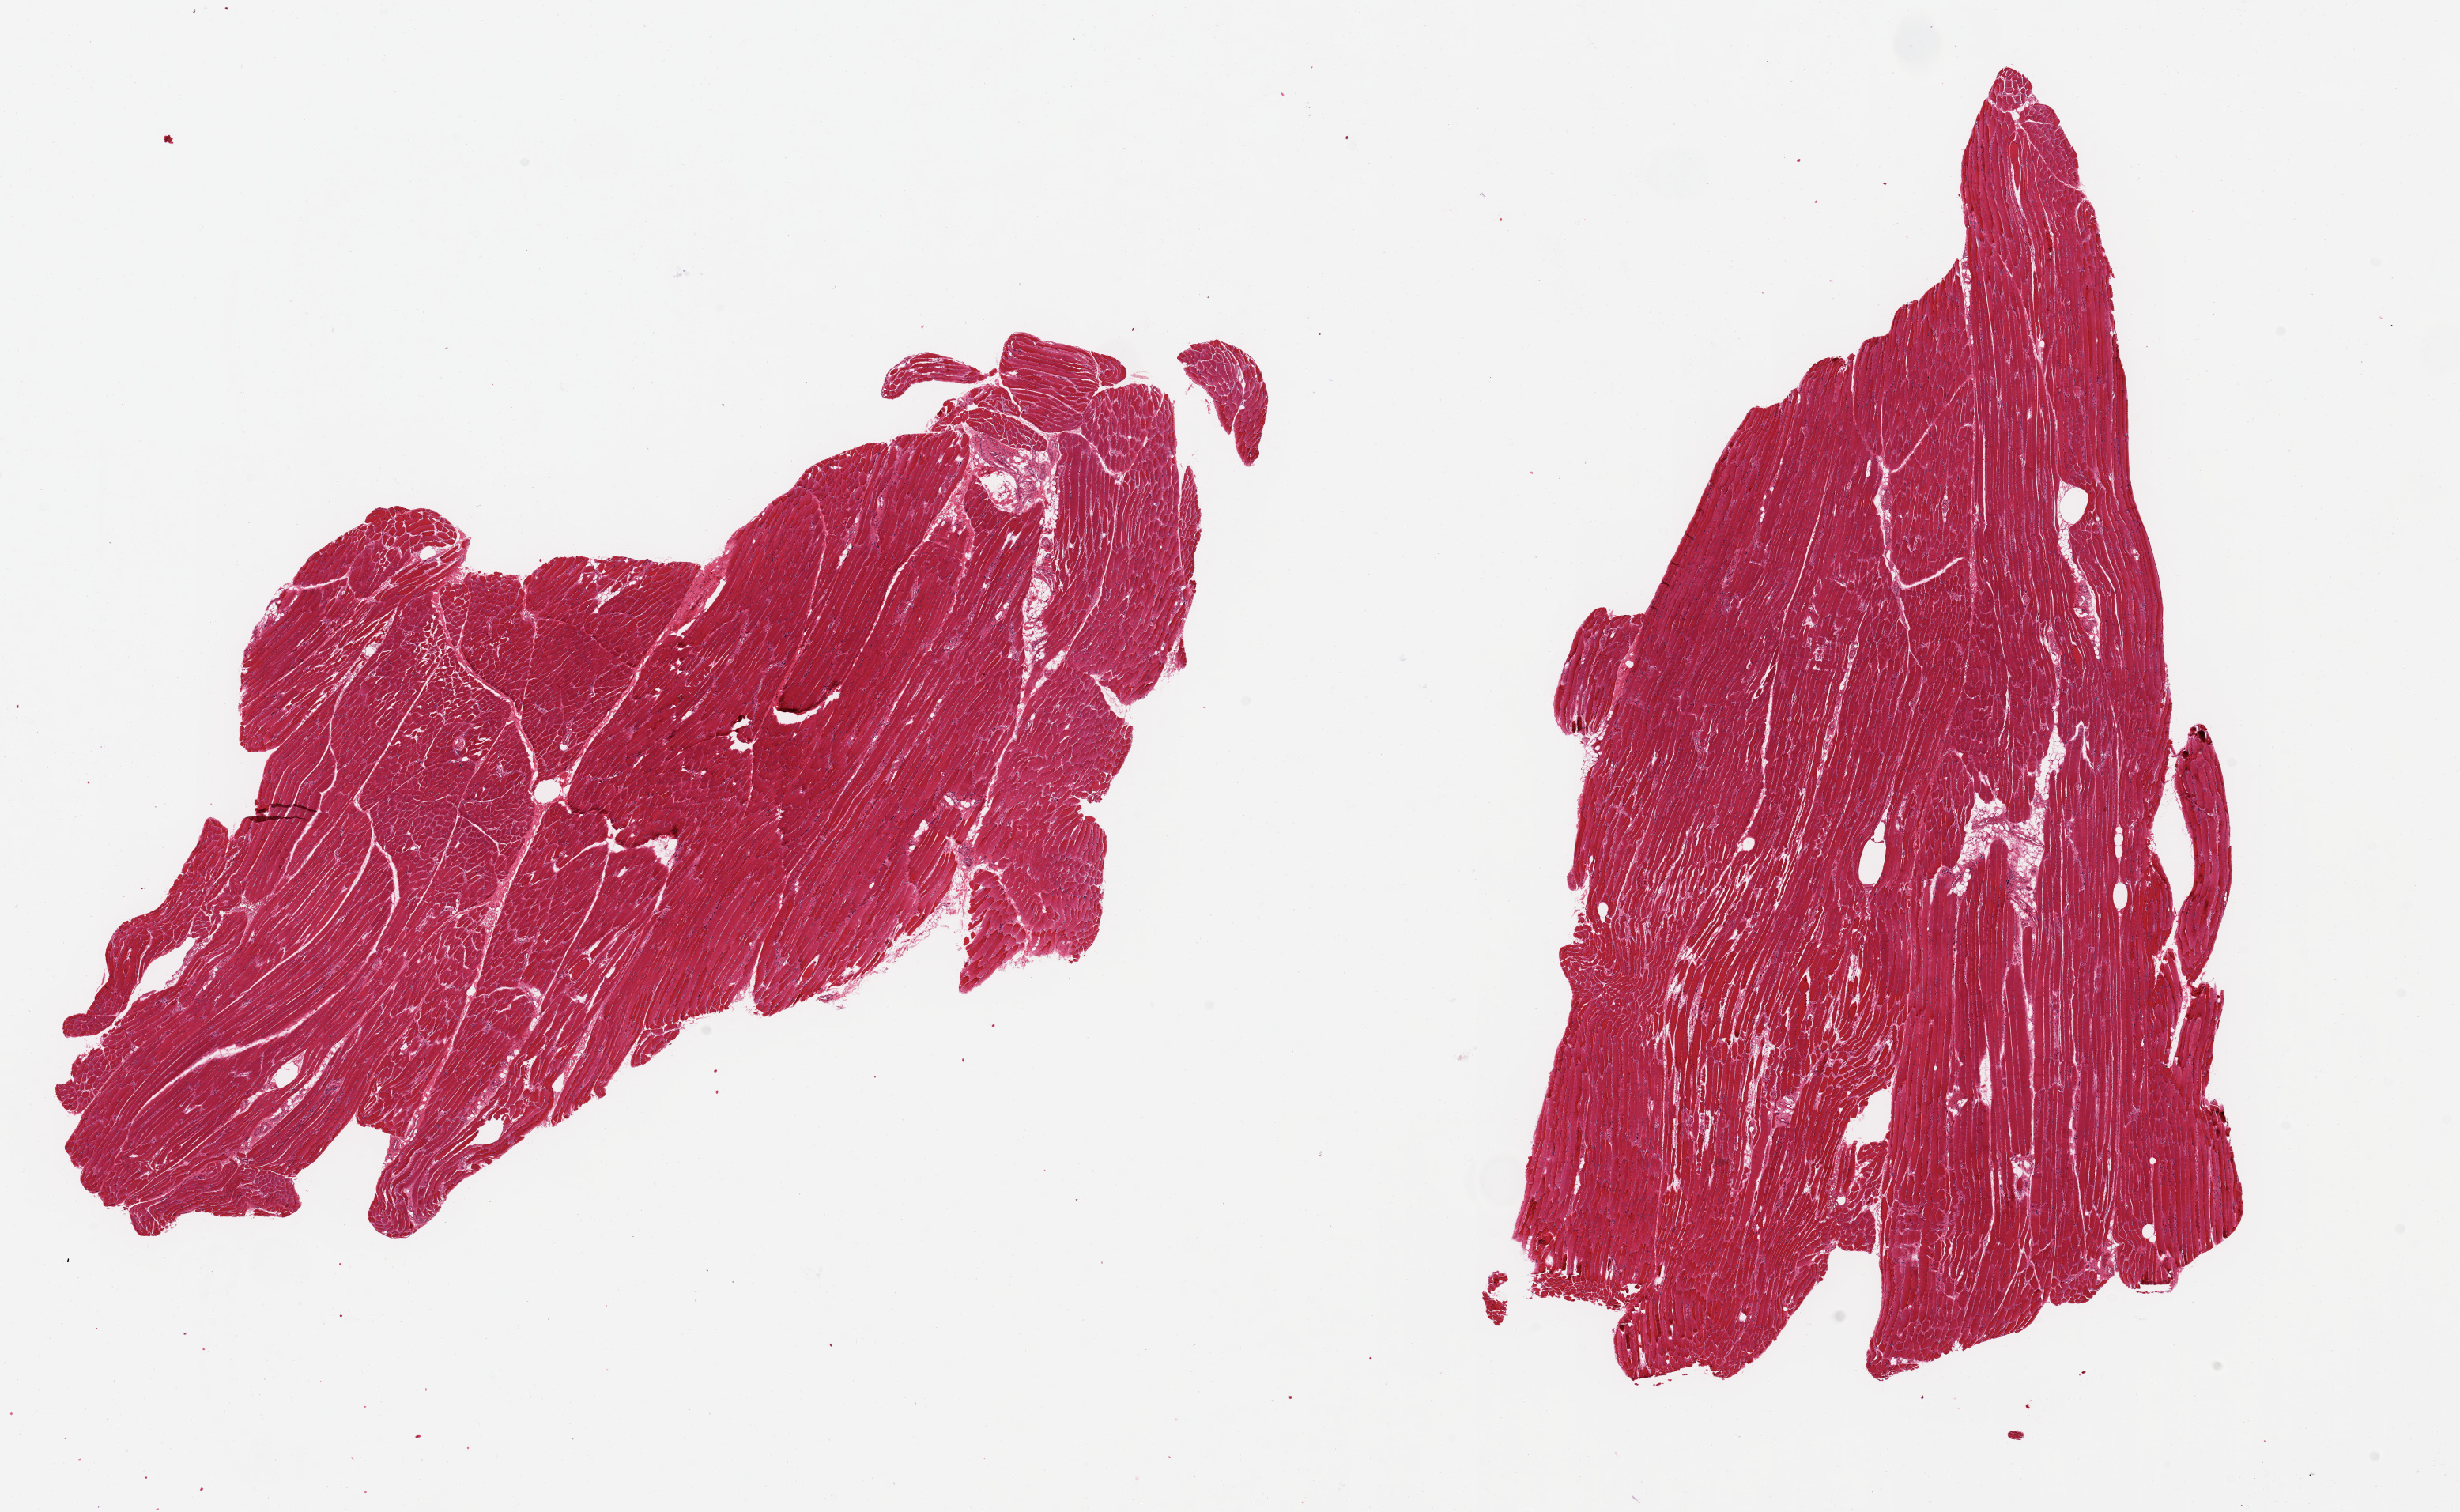
Haematoxylin and eosin whole-slide image, brightfield, shown as a low-resolution overview of the whole scanned area (about 24.6 x 15.1 mm); PAXgene-fixed paraffin-embedded (PFPE) section; sampled site (target tissue): skeletal muscle; tissue donor sample. Donor: female.
Reviewer comment on this tissue sample: 2 ~12x7mm aliquots, good clean specimens, <5% interstitial fat.